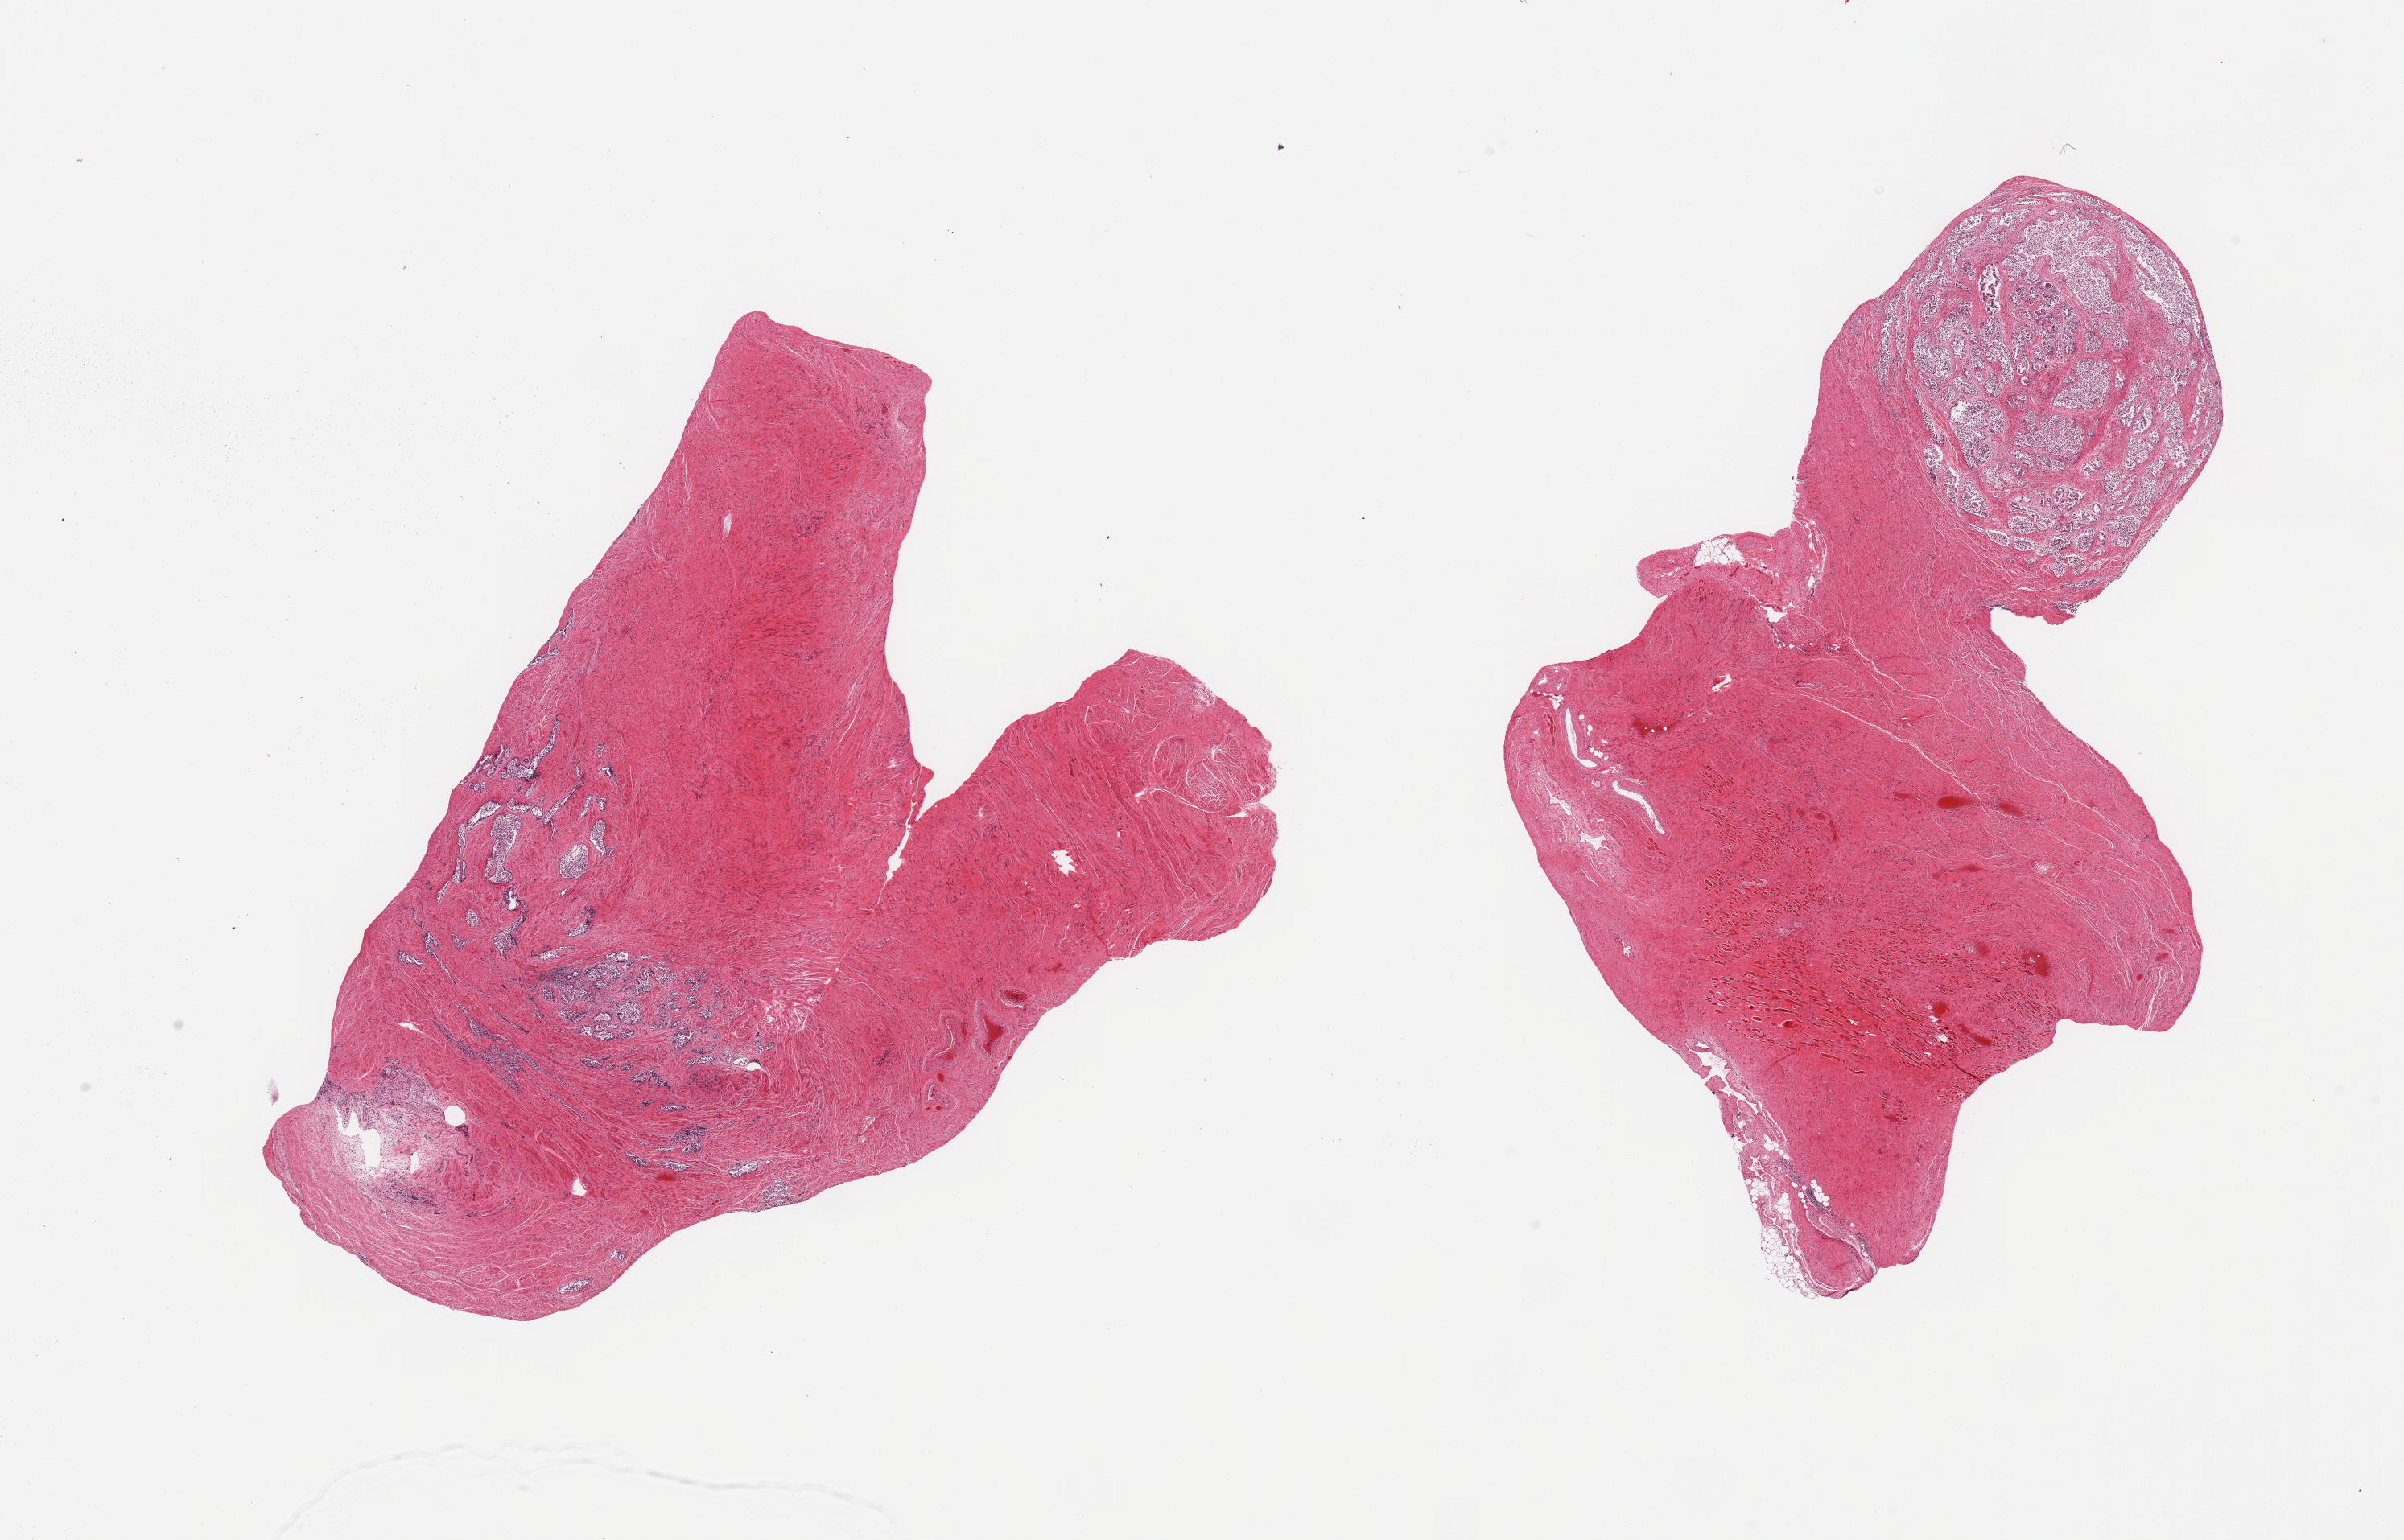
Hematoxylin and eosin (H&E) whole-slide image, brightfield, whole scanned area (about 23.6 x 15.1 mm) shown as a low-resolution overview. PAXgene-fixed, paraffin-embedded tissue. Sampled site (target tissue): prostate. Tissue donor sample. Donor: male.
Reviewer comment on this tissue sample: 2 pieces; one piece consists of fibromuscular stroma and glandular component (sloughed) and other consists of fibromuscular stroma and skeletal muscle with region of nodular glandular hyperplasia.